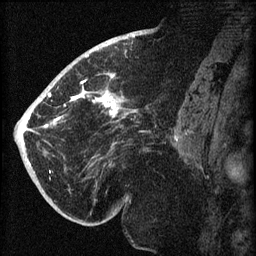
Breast MRI (dynamic contrast-enhanced), one sagittal slice; slice 38 of 60 in the series (ordered by position); dynamic contrast-enhanced series, image 2 of 3 at this slice position (ordered by acquisition); 1.5 T; TE 4.2 ms, TR 8.2 ms; 2 mm slice thickness; 256 × 256 image matrix. Female patient, age 71 years.
Outlined on this slice (semi-automatically segmented with operator editing):
- analysis volume of interest (the breast-tissue region the enhancement analysis was run in; not a lesion): bounding box [x1, y1, x2, y2] px = [40, 72, 148, 196]
- tumour enhancement mask (voxels above the 70 % enhancement threshold inside the analysis volume of interest): [44, 81, 118, 128]